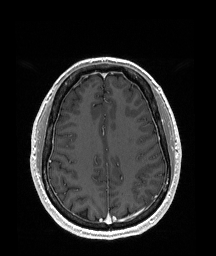
Brain MRI from a brain-tumour surgery series, one axial slice; position 68 of 192 along the scan axis; T1-weighted post-contrast; 1 mm slice thickness; 216 × 256 image matrix, field of view 219 × 260 mm. From the clinical record (not read from this slice): histopathology: Glioblastoma; WHO grade: 4; IDH mutation: no.
Annotated regions visible in this slice (expert manual segmentation):
- tumour: box from (x=152, y=197) to (x=155, y=200) px